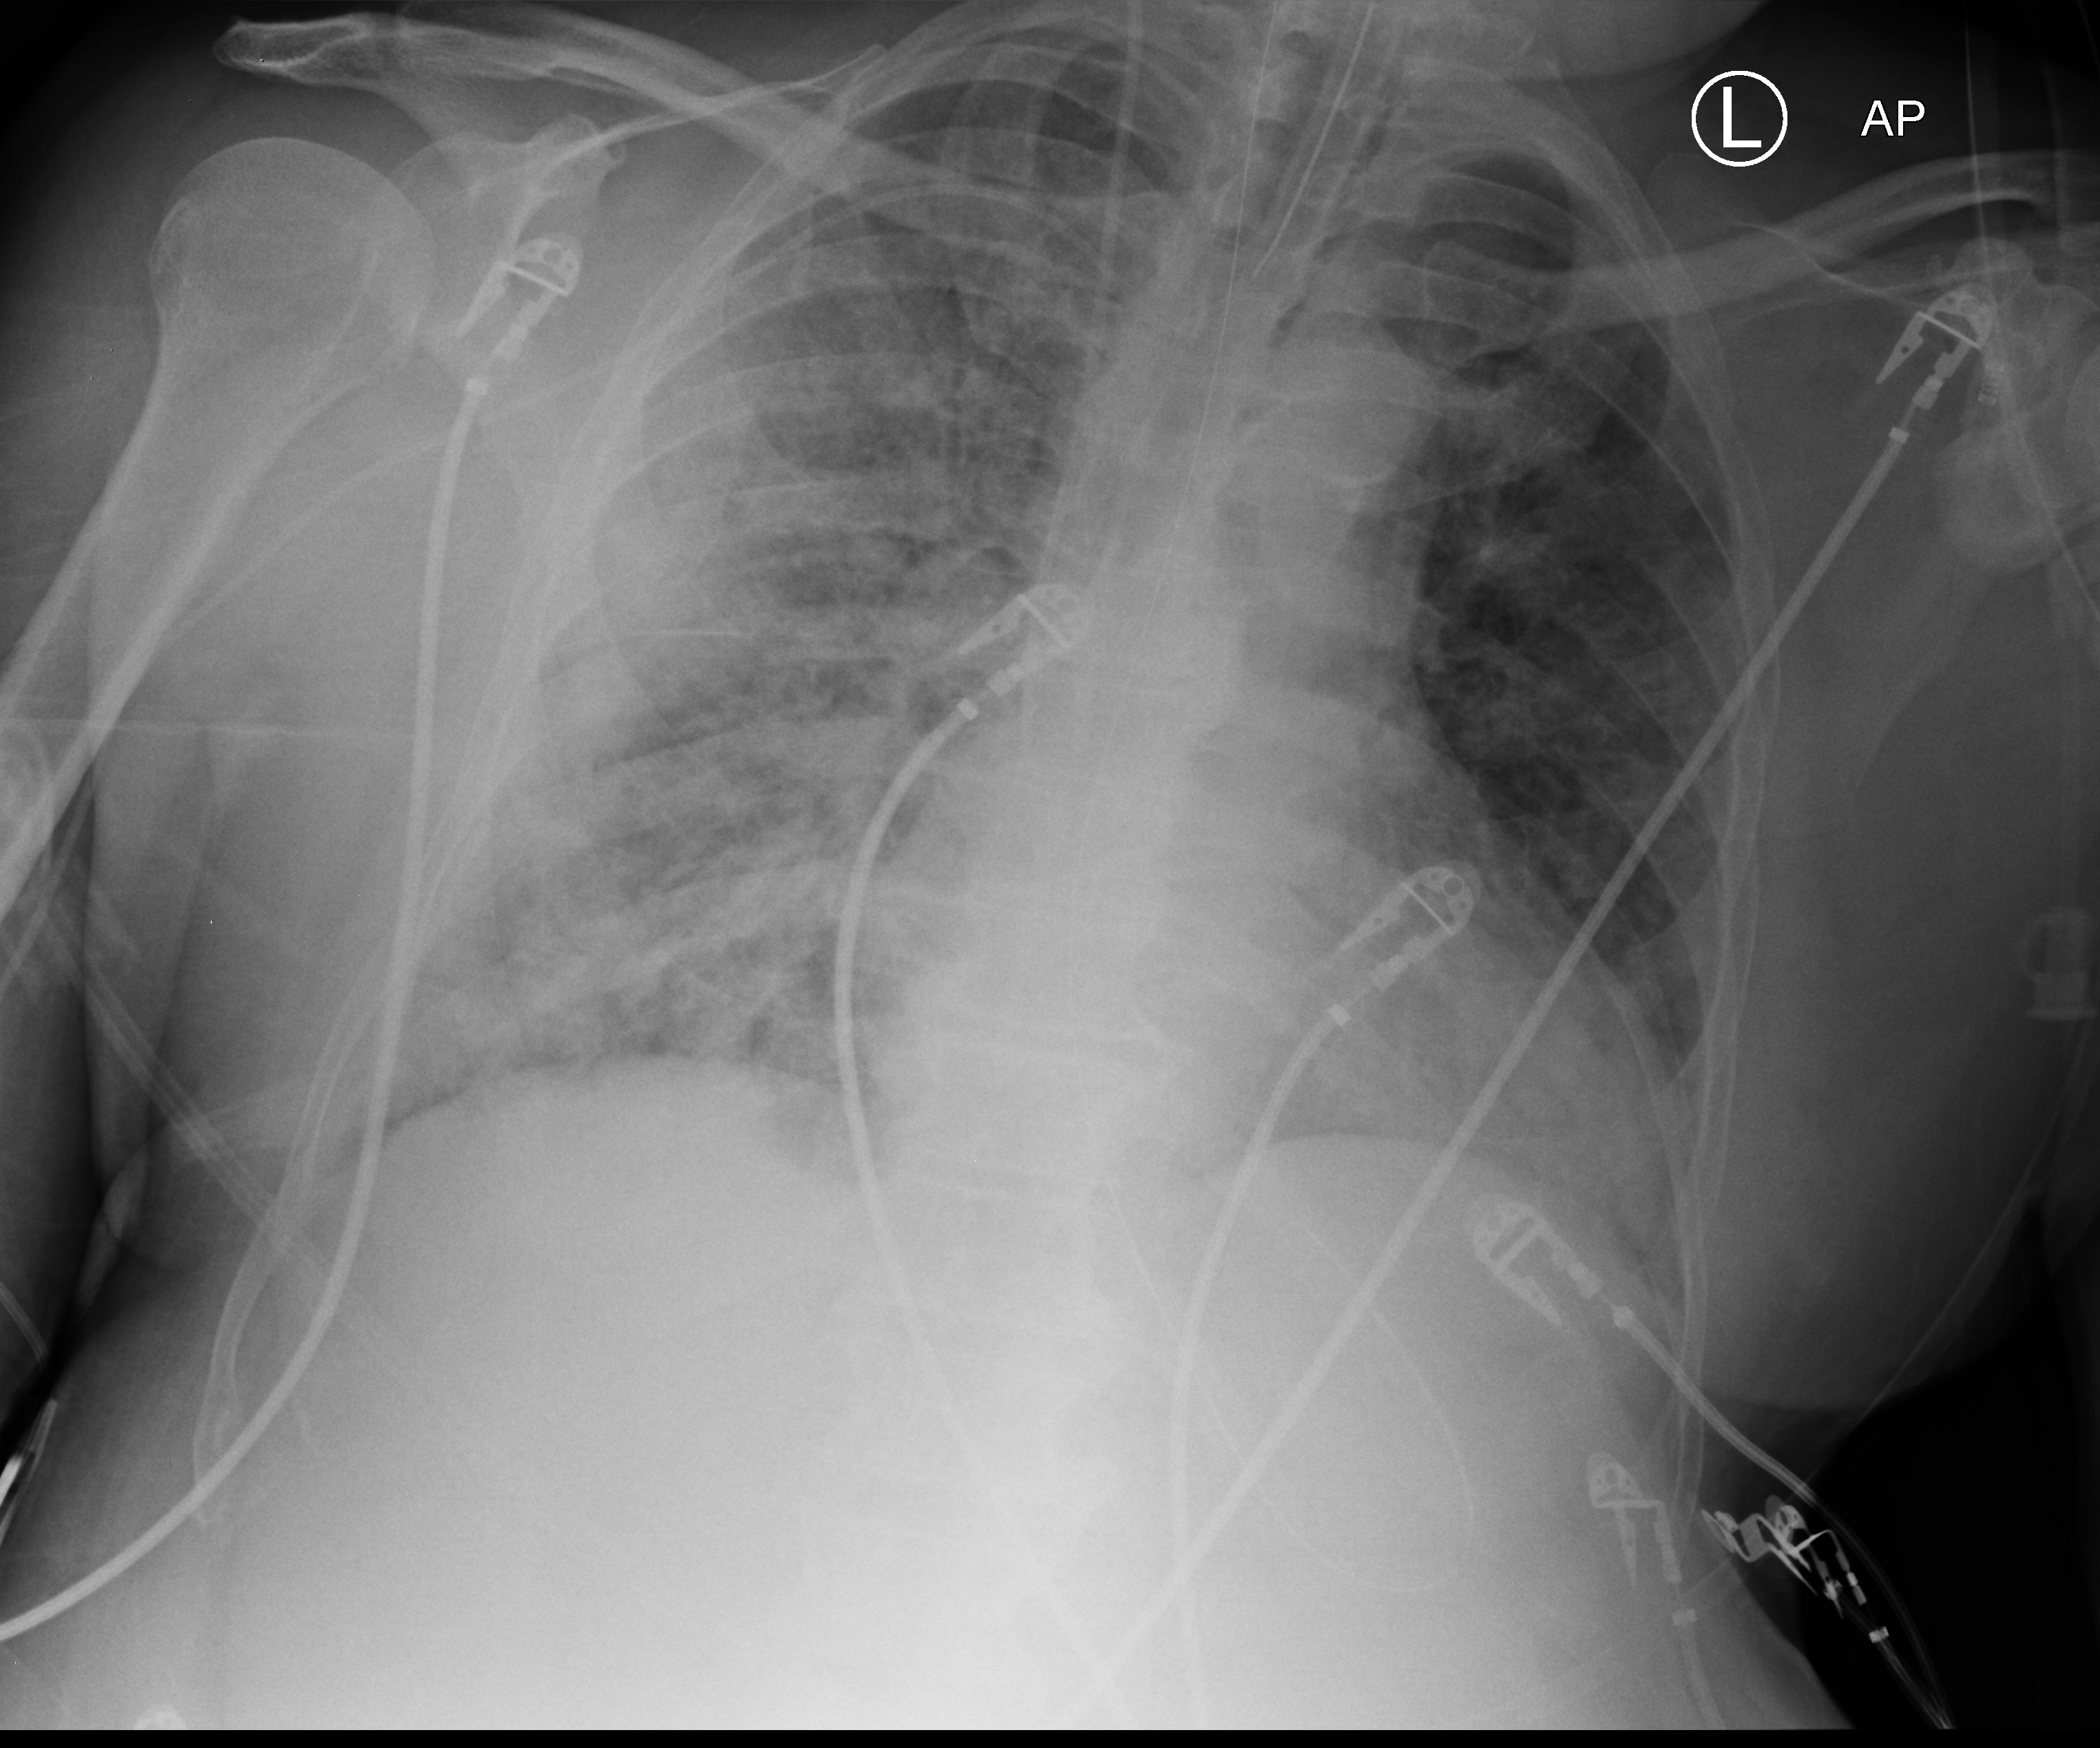
Bedside chest radiograph (computed radiography); anteroposterior (AP) projection. Patient hospitalised with COVID-19; male, aged 60–74 years.
From the hospital-stay record, not from the radiograph (when in the stay this image was taken is not recorded): mechanically ventilated during this hospital stay: yes; admitted to intensive care during this hospital stay: yes.